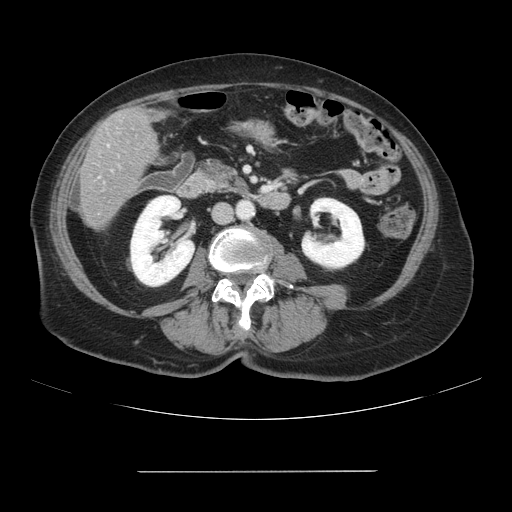
Contrast-enhanced abdominal CT, one axial slice. Position 17 of 111 along the scan axis. 120 kVp. Soft-tissue window (W 400 / L 40 HU). 2.5 mm slice thickness. 512 × 512 image matrix, field of view 400 × 400 mm. Female patient, age 74 years. Case-level facts recorded for this patient, not image findings: diagnosis: colorectal cancer liver metastases, imaged before liver resection; multiple liver metastases: yes; largest metastasis: 1.1 cm.
Structures marked on this image (outlined manually by an expert reader):
- liver: bounding box <80,106,160,230> (left, top, right, bottom; pixels)